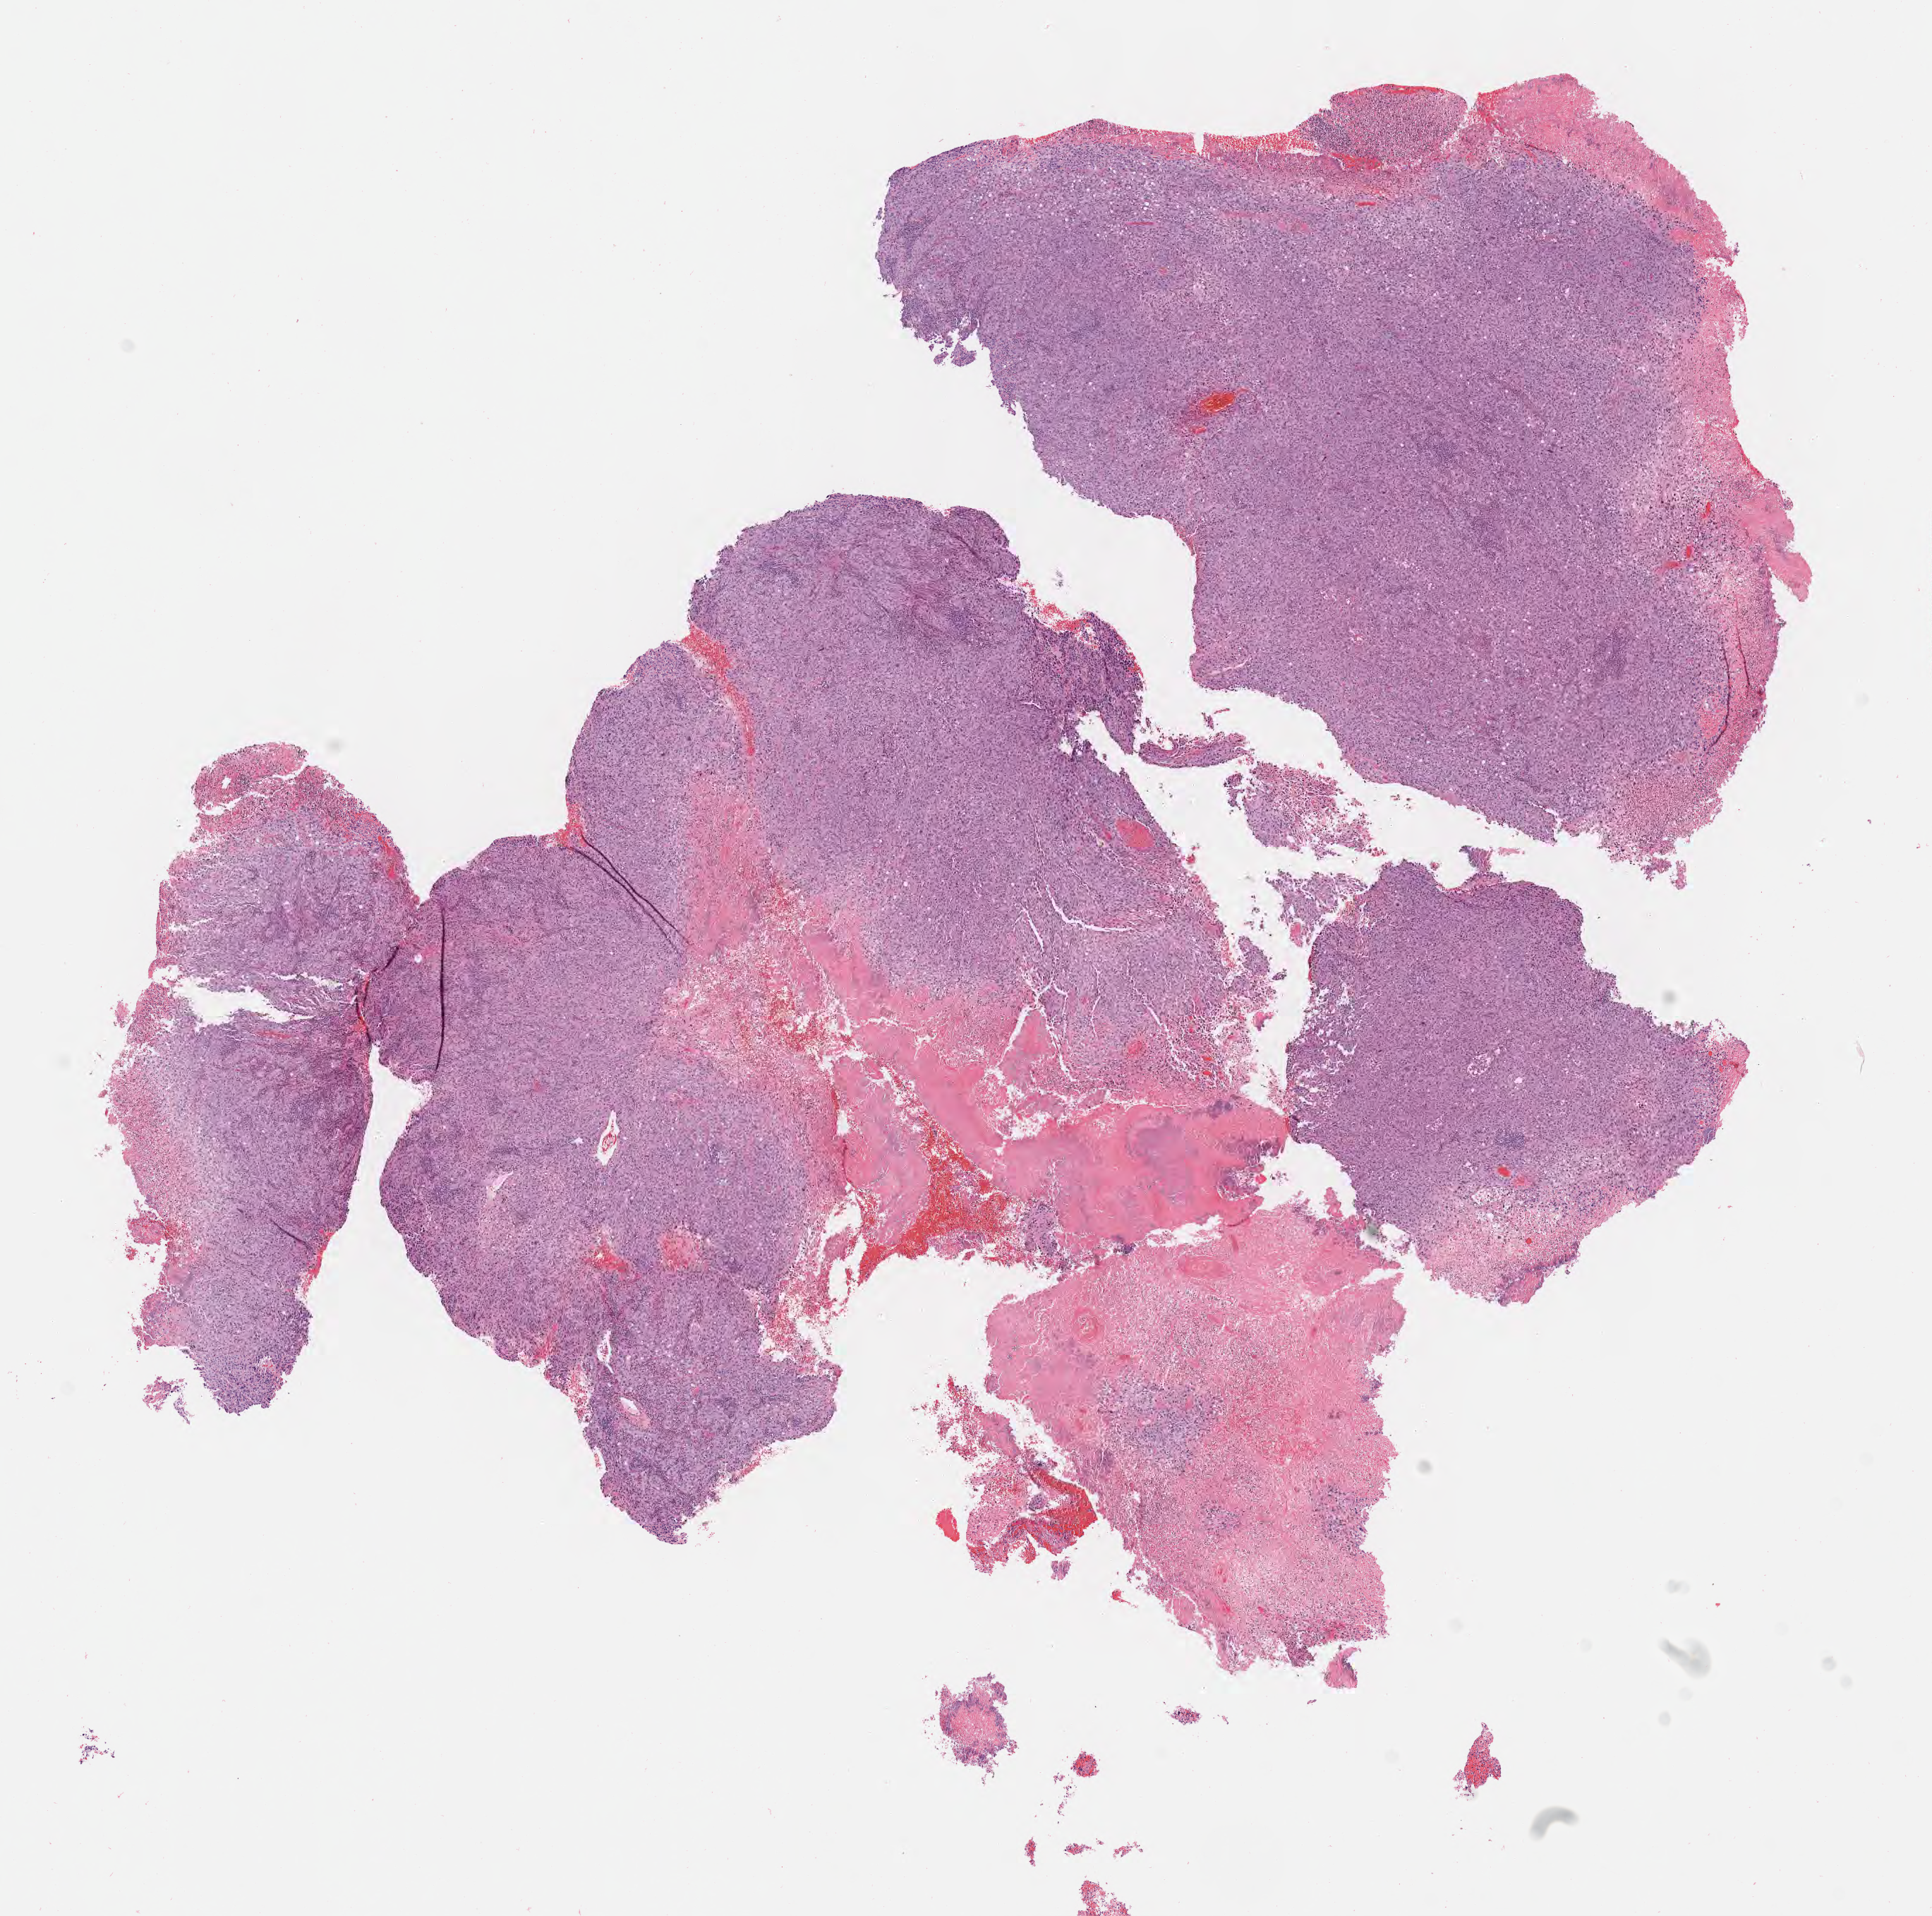
H&E whole-slide image, a low-resolution overview of the entire scanned area, about 11.1 x 11.0 mm; tumor tissue; anatomic site: cervix. Patient: female, aged 48.
Histologic diagnosis: Squamous cell carcinoma, large cell, nonkeratinizing, NOS.